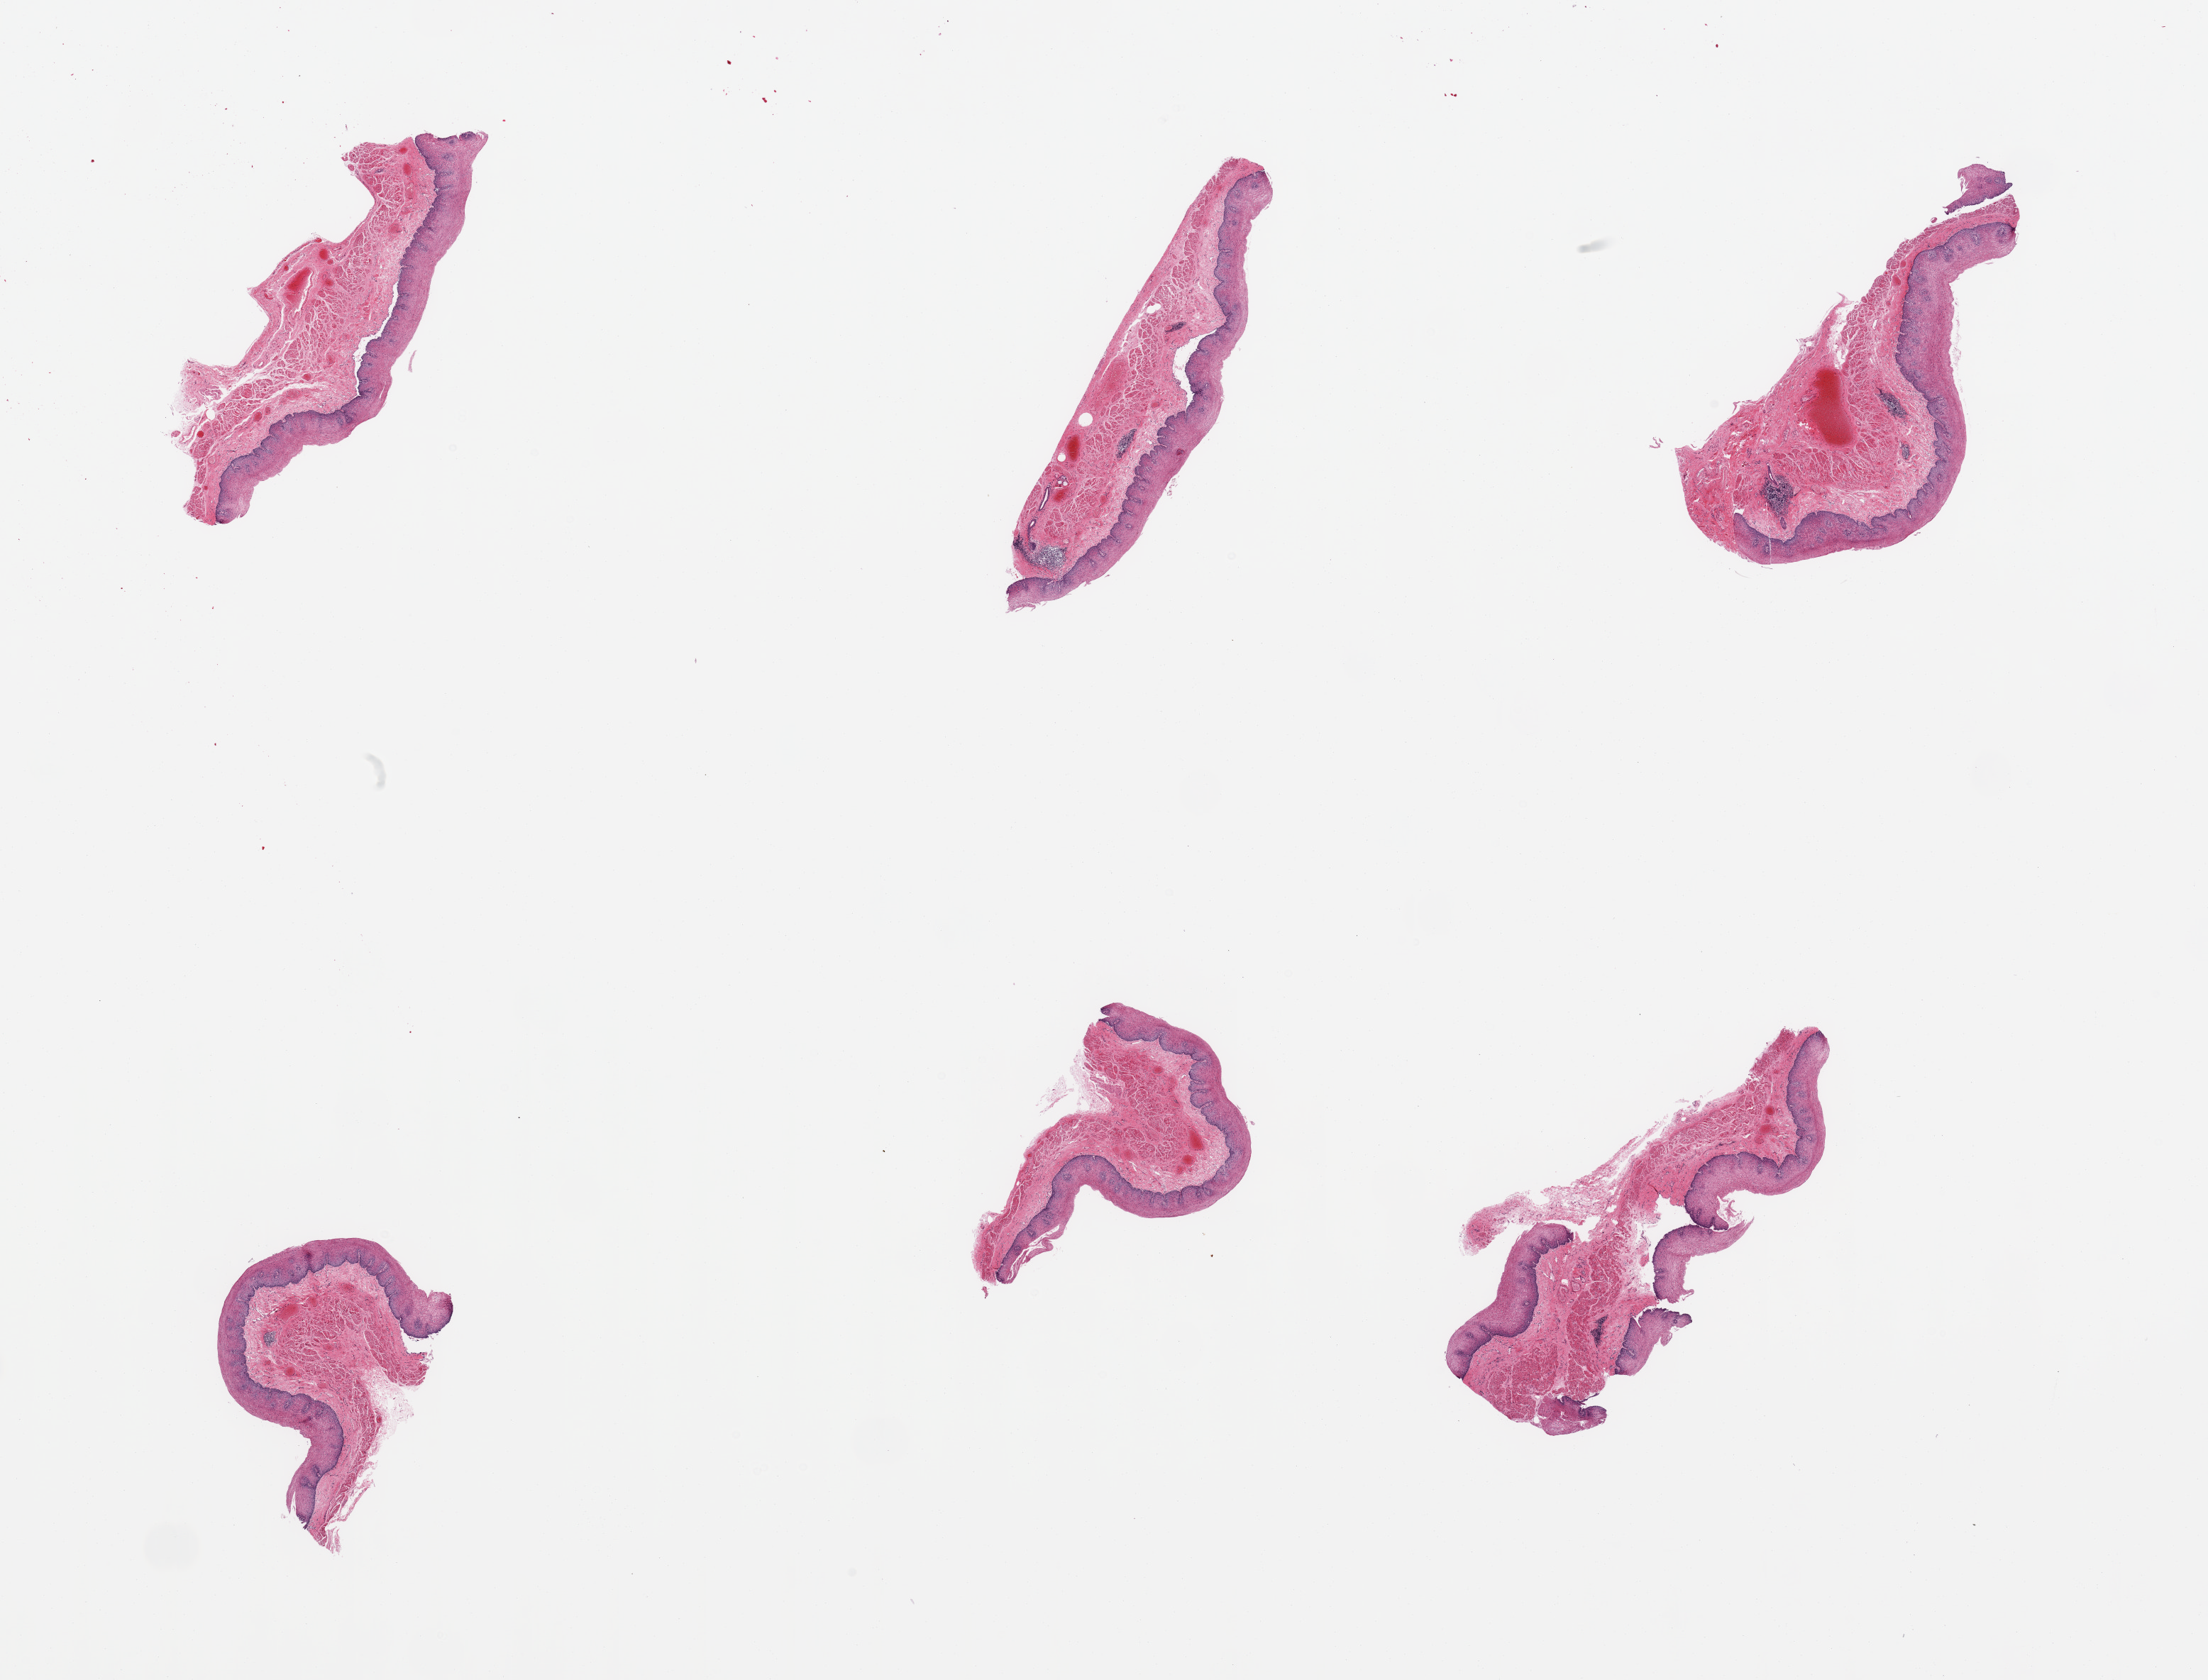
Whole-slide image, H&E stain, a low-resolution overview of the entire scanned area, about 24.6 x 18.7 mm. PAXgene-fixed paraffin-embedded (PFPE) section. Sampled site (target tissue): esophageal mucous membrane. Donor tissue sample. Male donor.
• reviewer comment on this tissue sample: 6 pieces, squamous mucosa with early separation, up to ~0.4mm, 20-30% of thickness